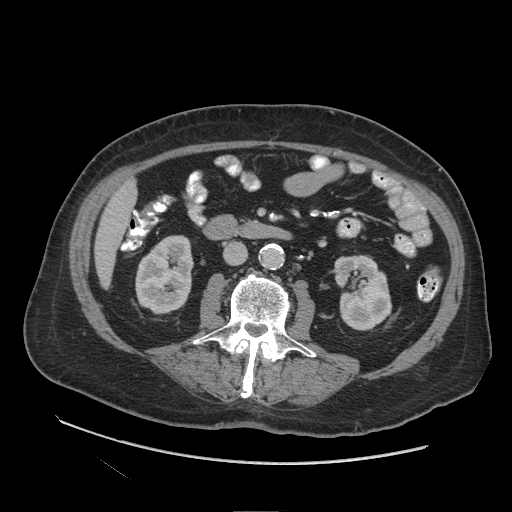
Contrast-enhanced abdominal CT (liver protocol), one axial slice. Position 26 of 109 along the scan axis. Reconstruction kernel STANDARD. 140 kVp. Soft-tissue window (W 400 / L 40 HU). 2.5 mm slice thickness. 512 × 512 image matrix, field of view 420 × 420 mm. Case-level facts recorded for this patient, not image findings: diagnosis: hepatocellular carcinoma (patient treated with transarterial chemoembolisation; whether this scan precedes or follows treatment is not stated here); TNM stage (as recorded): Stage-I; Child-Pugh class: A.
Outlined on this slice (semi-automatically segmented with operator editing):
- liver parenchyma outside the tumour (the mass and vessels are separate outlines, so this box may not span the whole liver): box from (x=94, y=179) to (x=136, y=287) px